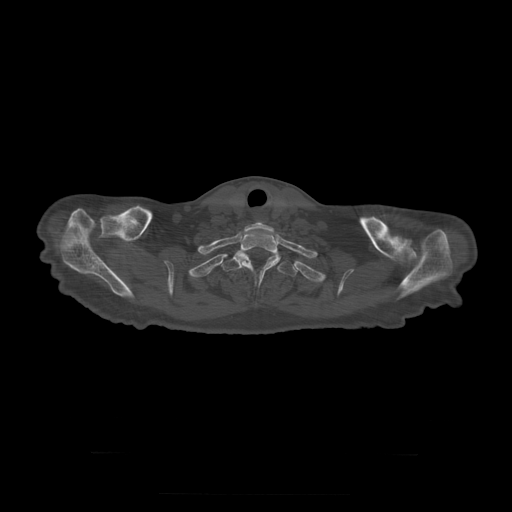
CT including the spine, one axial slice. Reconstruction kernel STANDARD. 120 kVp. Bone window (W 1800 / L 400 HU). 512 × 512 image matrix. Patient age 73 years. Case-level facts recorded for this patient, not image findings: primary cancer: prostate.
Outlined on this slice (semi-automatically segmented with operator editing):
- T1 vertebra: bounding box (x1, y1, x2, y2) in pixels: (235, 231, 281, 281)
- T2 vertebra: (222, 255, 298, 277)